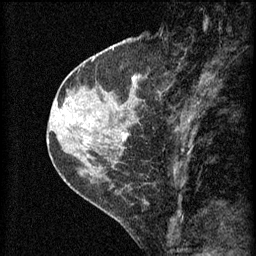
Breast MRI (dynamic contrast-enhanced), one sagittal slice; slice 23 of 60 in the series (ordered by position); 3 images stored at this slice position (order not interpretable as contrast timing); 1.5 T; TE 4.2 ms, TR 8.2 ms; 2 mm slice thickness; 256 × 256 image matrix. Patient: female, 45 years.
Annotated regions visible in this slice (semi-automatic segmentation, software-assisted and operator-edited):
- analysis volume of interest (the breast-tissue region the enhancement analysis was run in; not a lesion): bounding box [x1, y1, x2, y2] px = [62, 98, 104, 139]
- tumour enhancement mask (voxels above the 70 % enhancement threshold inside the analysis volume of interest): [65, 98, 73, 107]